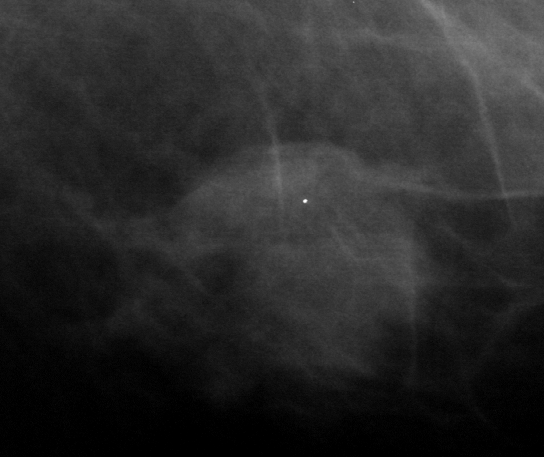
Region of interest cut from a scanned film mammogram (one marked finding), left breast, MLO view.
- Mass, shape lobulated, margins microlobulated; BI-RADS assessment category 5; subtlety rating 5 on a 1 (subtle) to 5 (obvious) scale; pathology (as recorded): malignant.